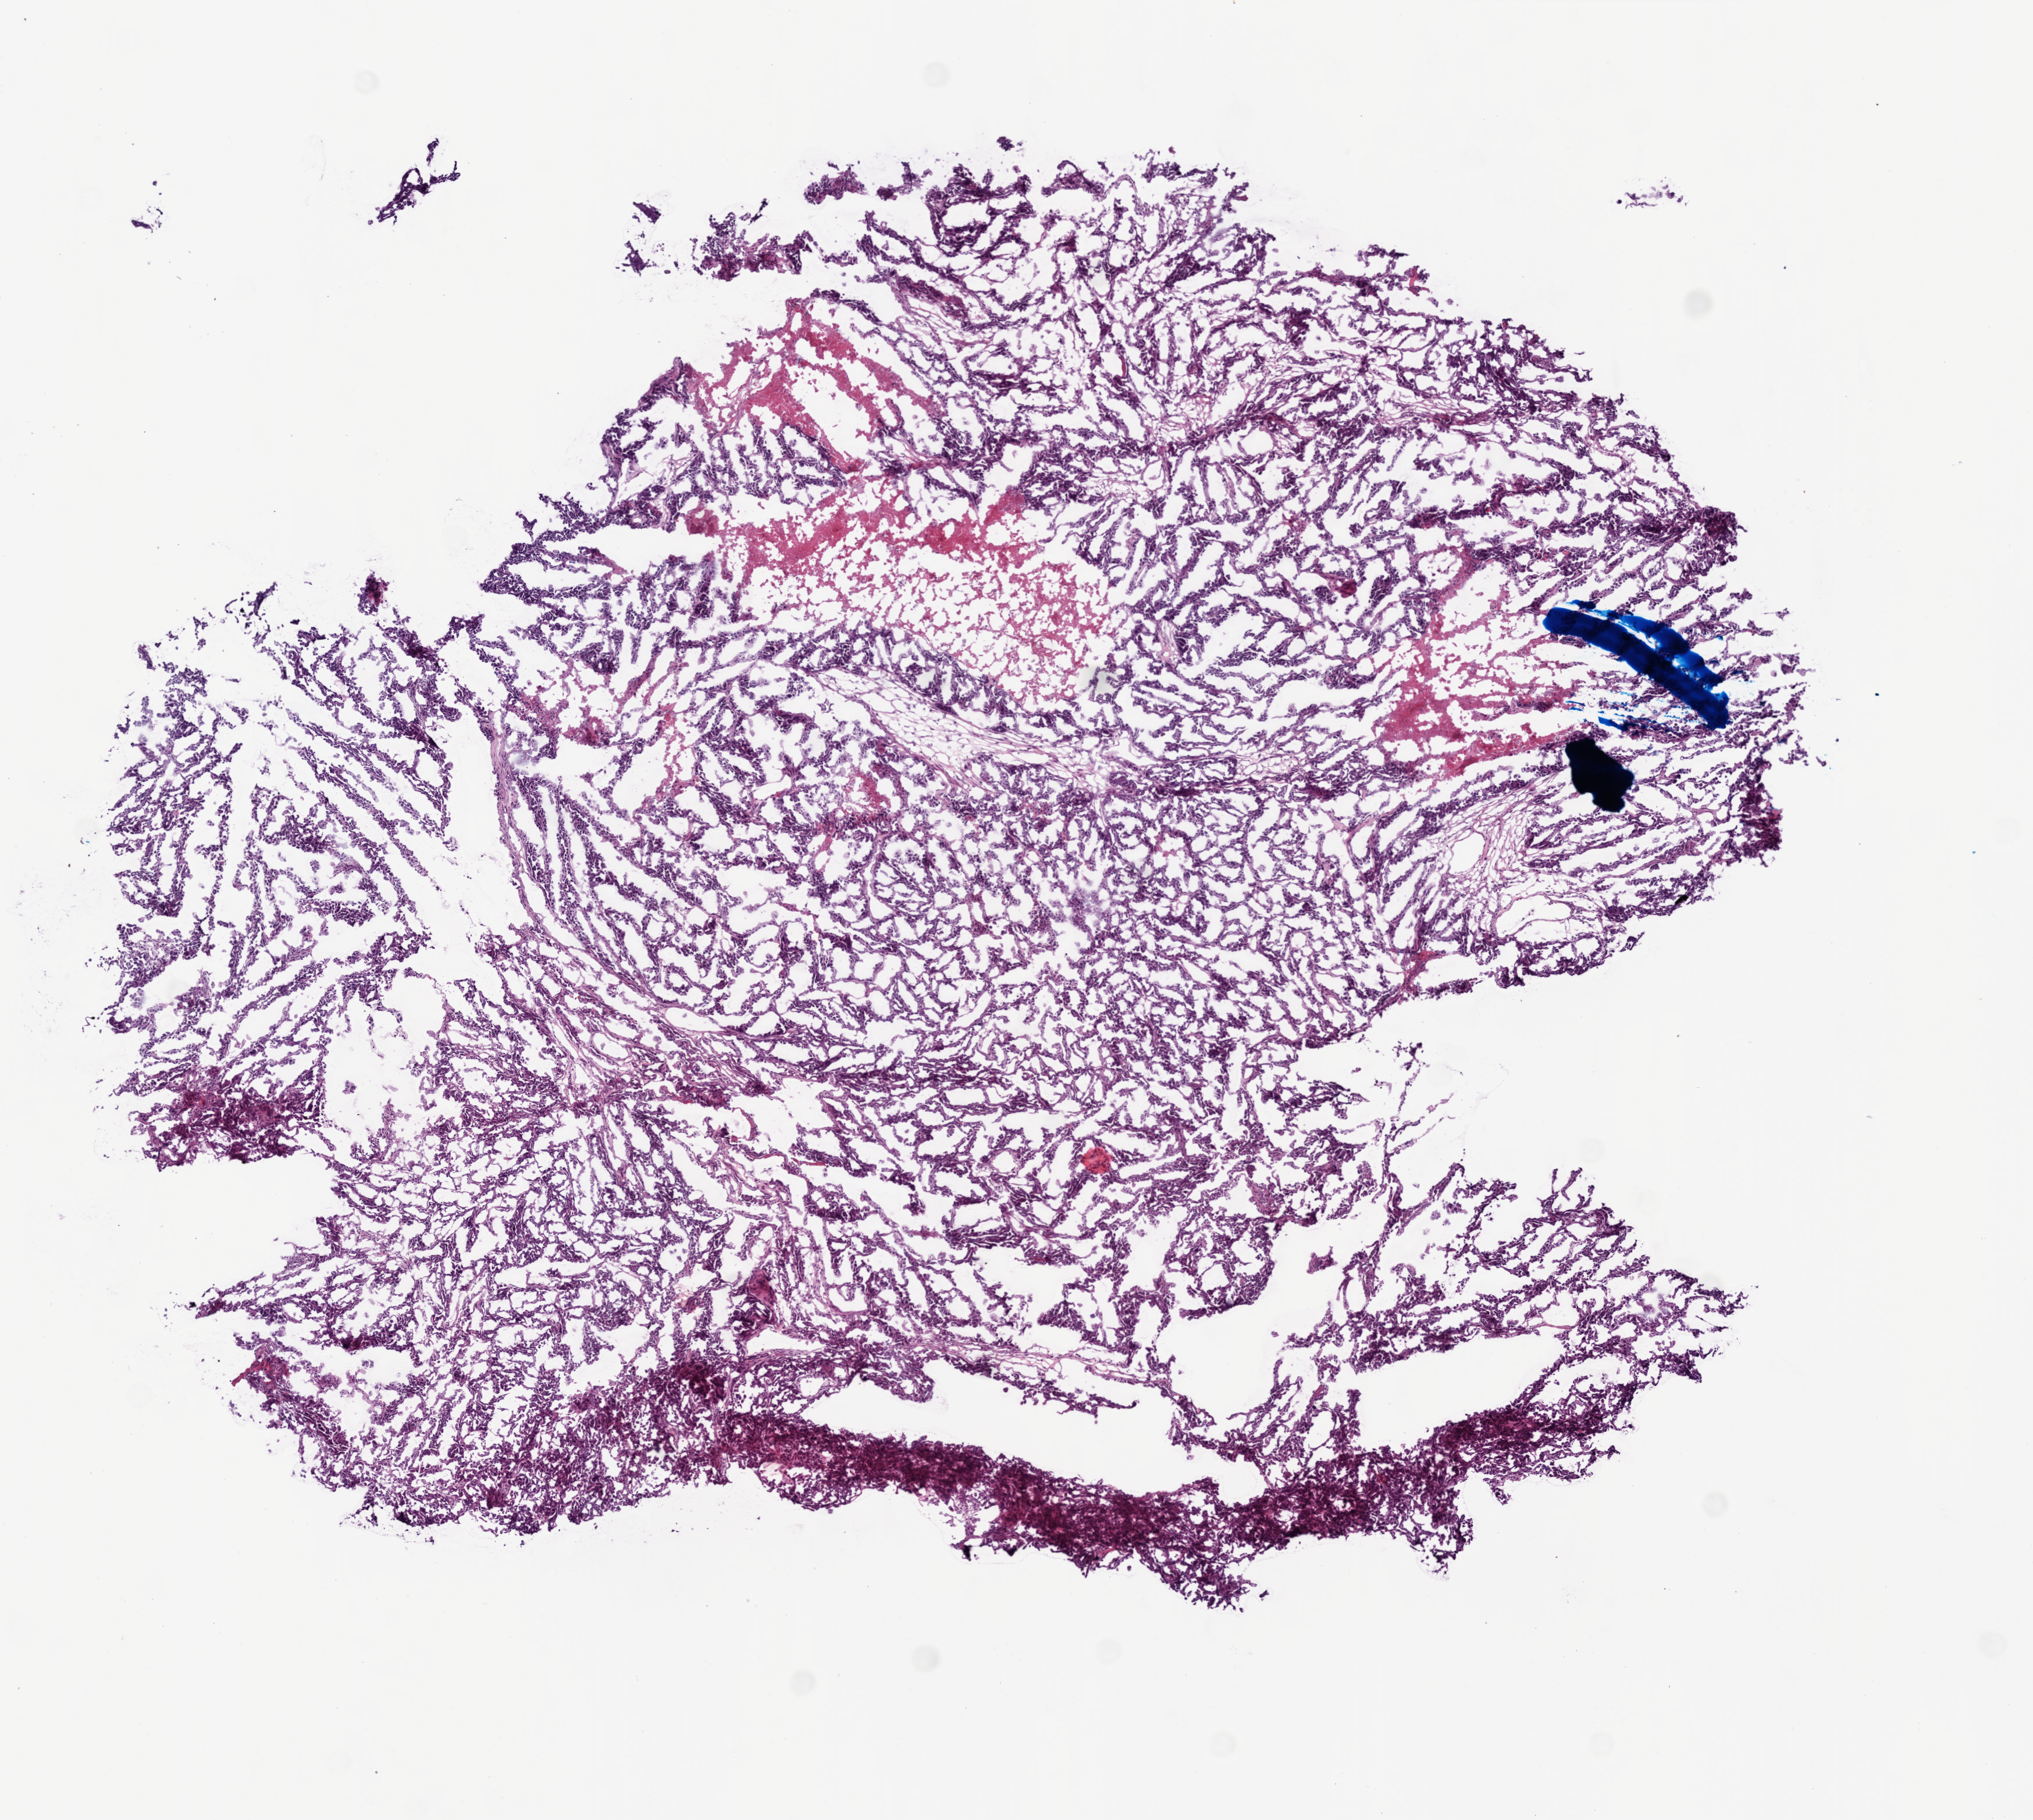
Whole-slide histology image, H&E, shown as a low-resolution overview of the whole scanned area (about 7.0 x 6.3 mm, acquisition: 20x scan); frozen section from the top of the tissue portion; sample: primary tumour, ovary. Patient: female, age at initial diagnosis 62 years. Histologic grade: G3 (poorly differentiated). Pathologist review of this section (percent, as recorded): tumour cells 0%, tumour nuclei 90%, normal cells 0%, stromal cells 0%, necrosis 10%.
Laterality: left. FIGO stage: IIIC. Pathologic diagnosis: Serous cystadenocarcinoma, NOS.